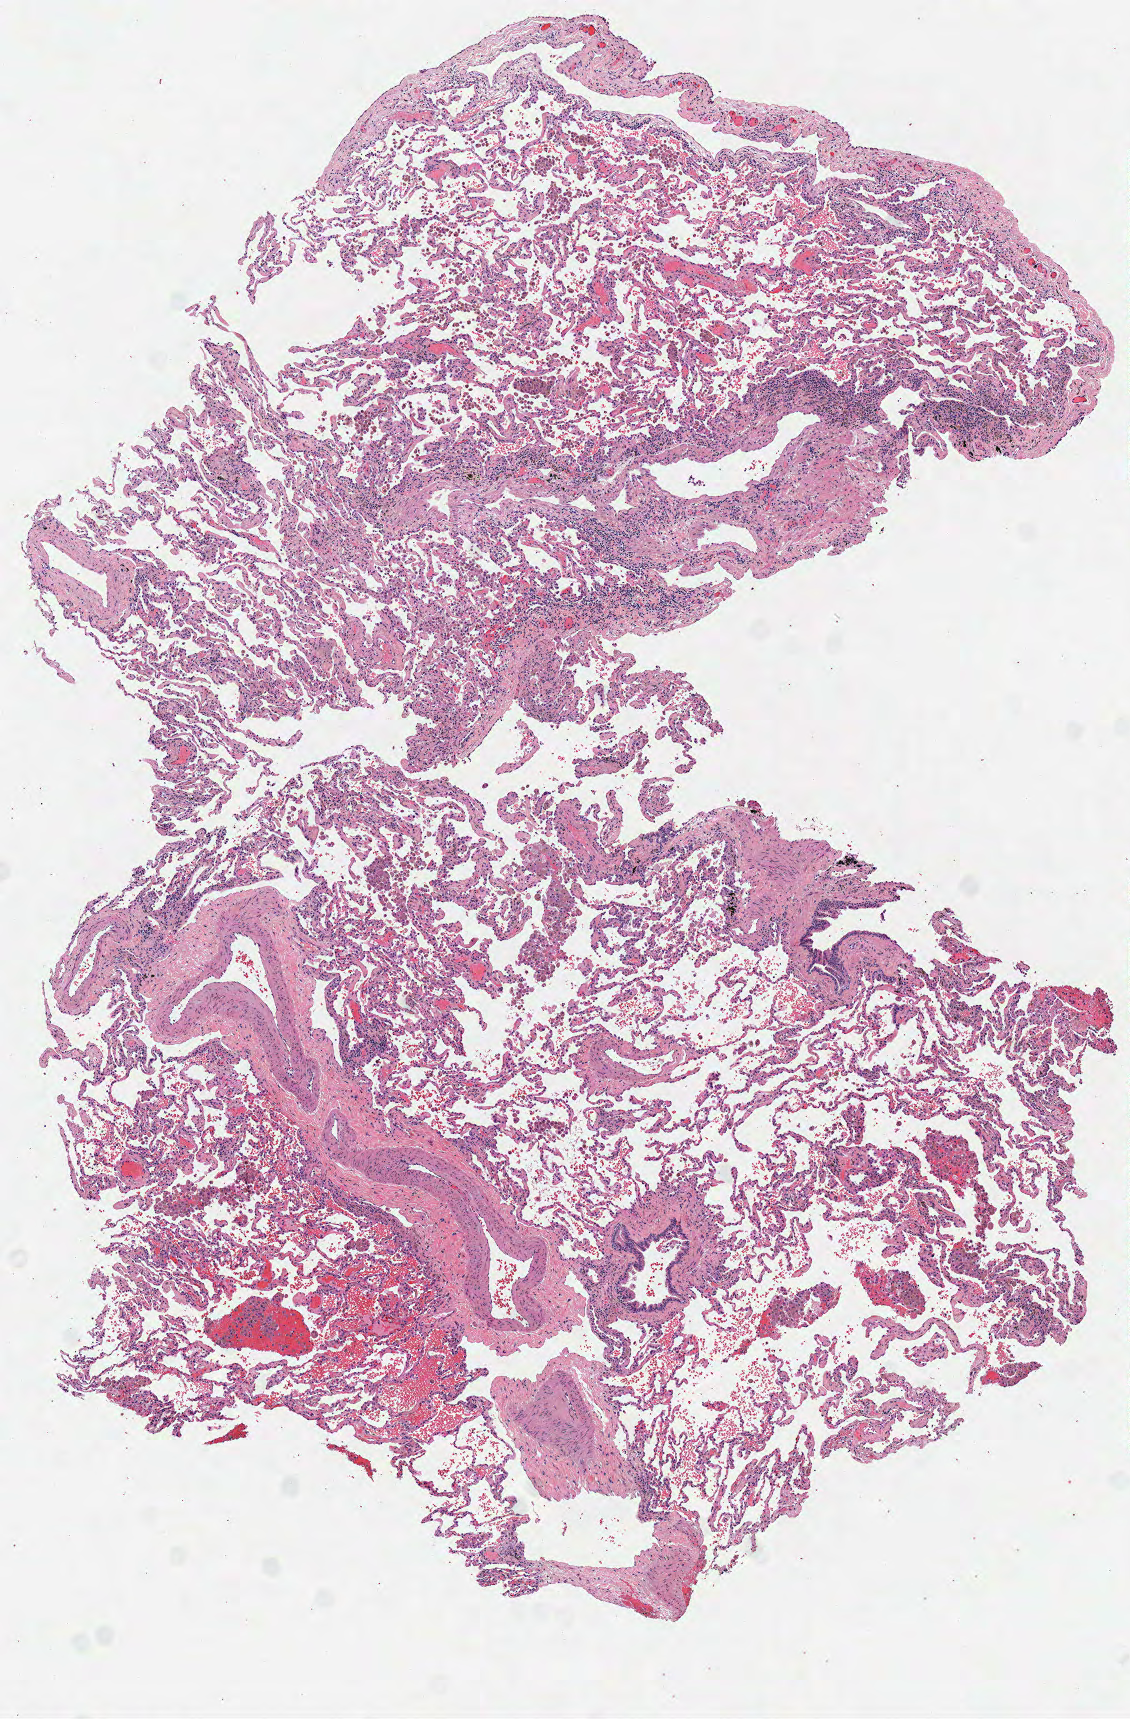
Hematoxylin and eosin (H&E) stained whole-slide image, low-resolution overview of the scanned area, about 4.5 x 6.8 mm; frozen section from the top of the tissue portion; solid tissue normal (non-tumour tissue) sample from the lung. Female patient; age at initial diagnosis 52 years.
* this section: solid tissue normal sample (biorepository sample class)
* patient diagnosis: Adenocarcinoma, NOS